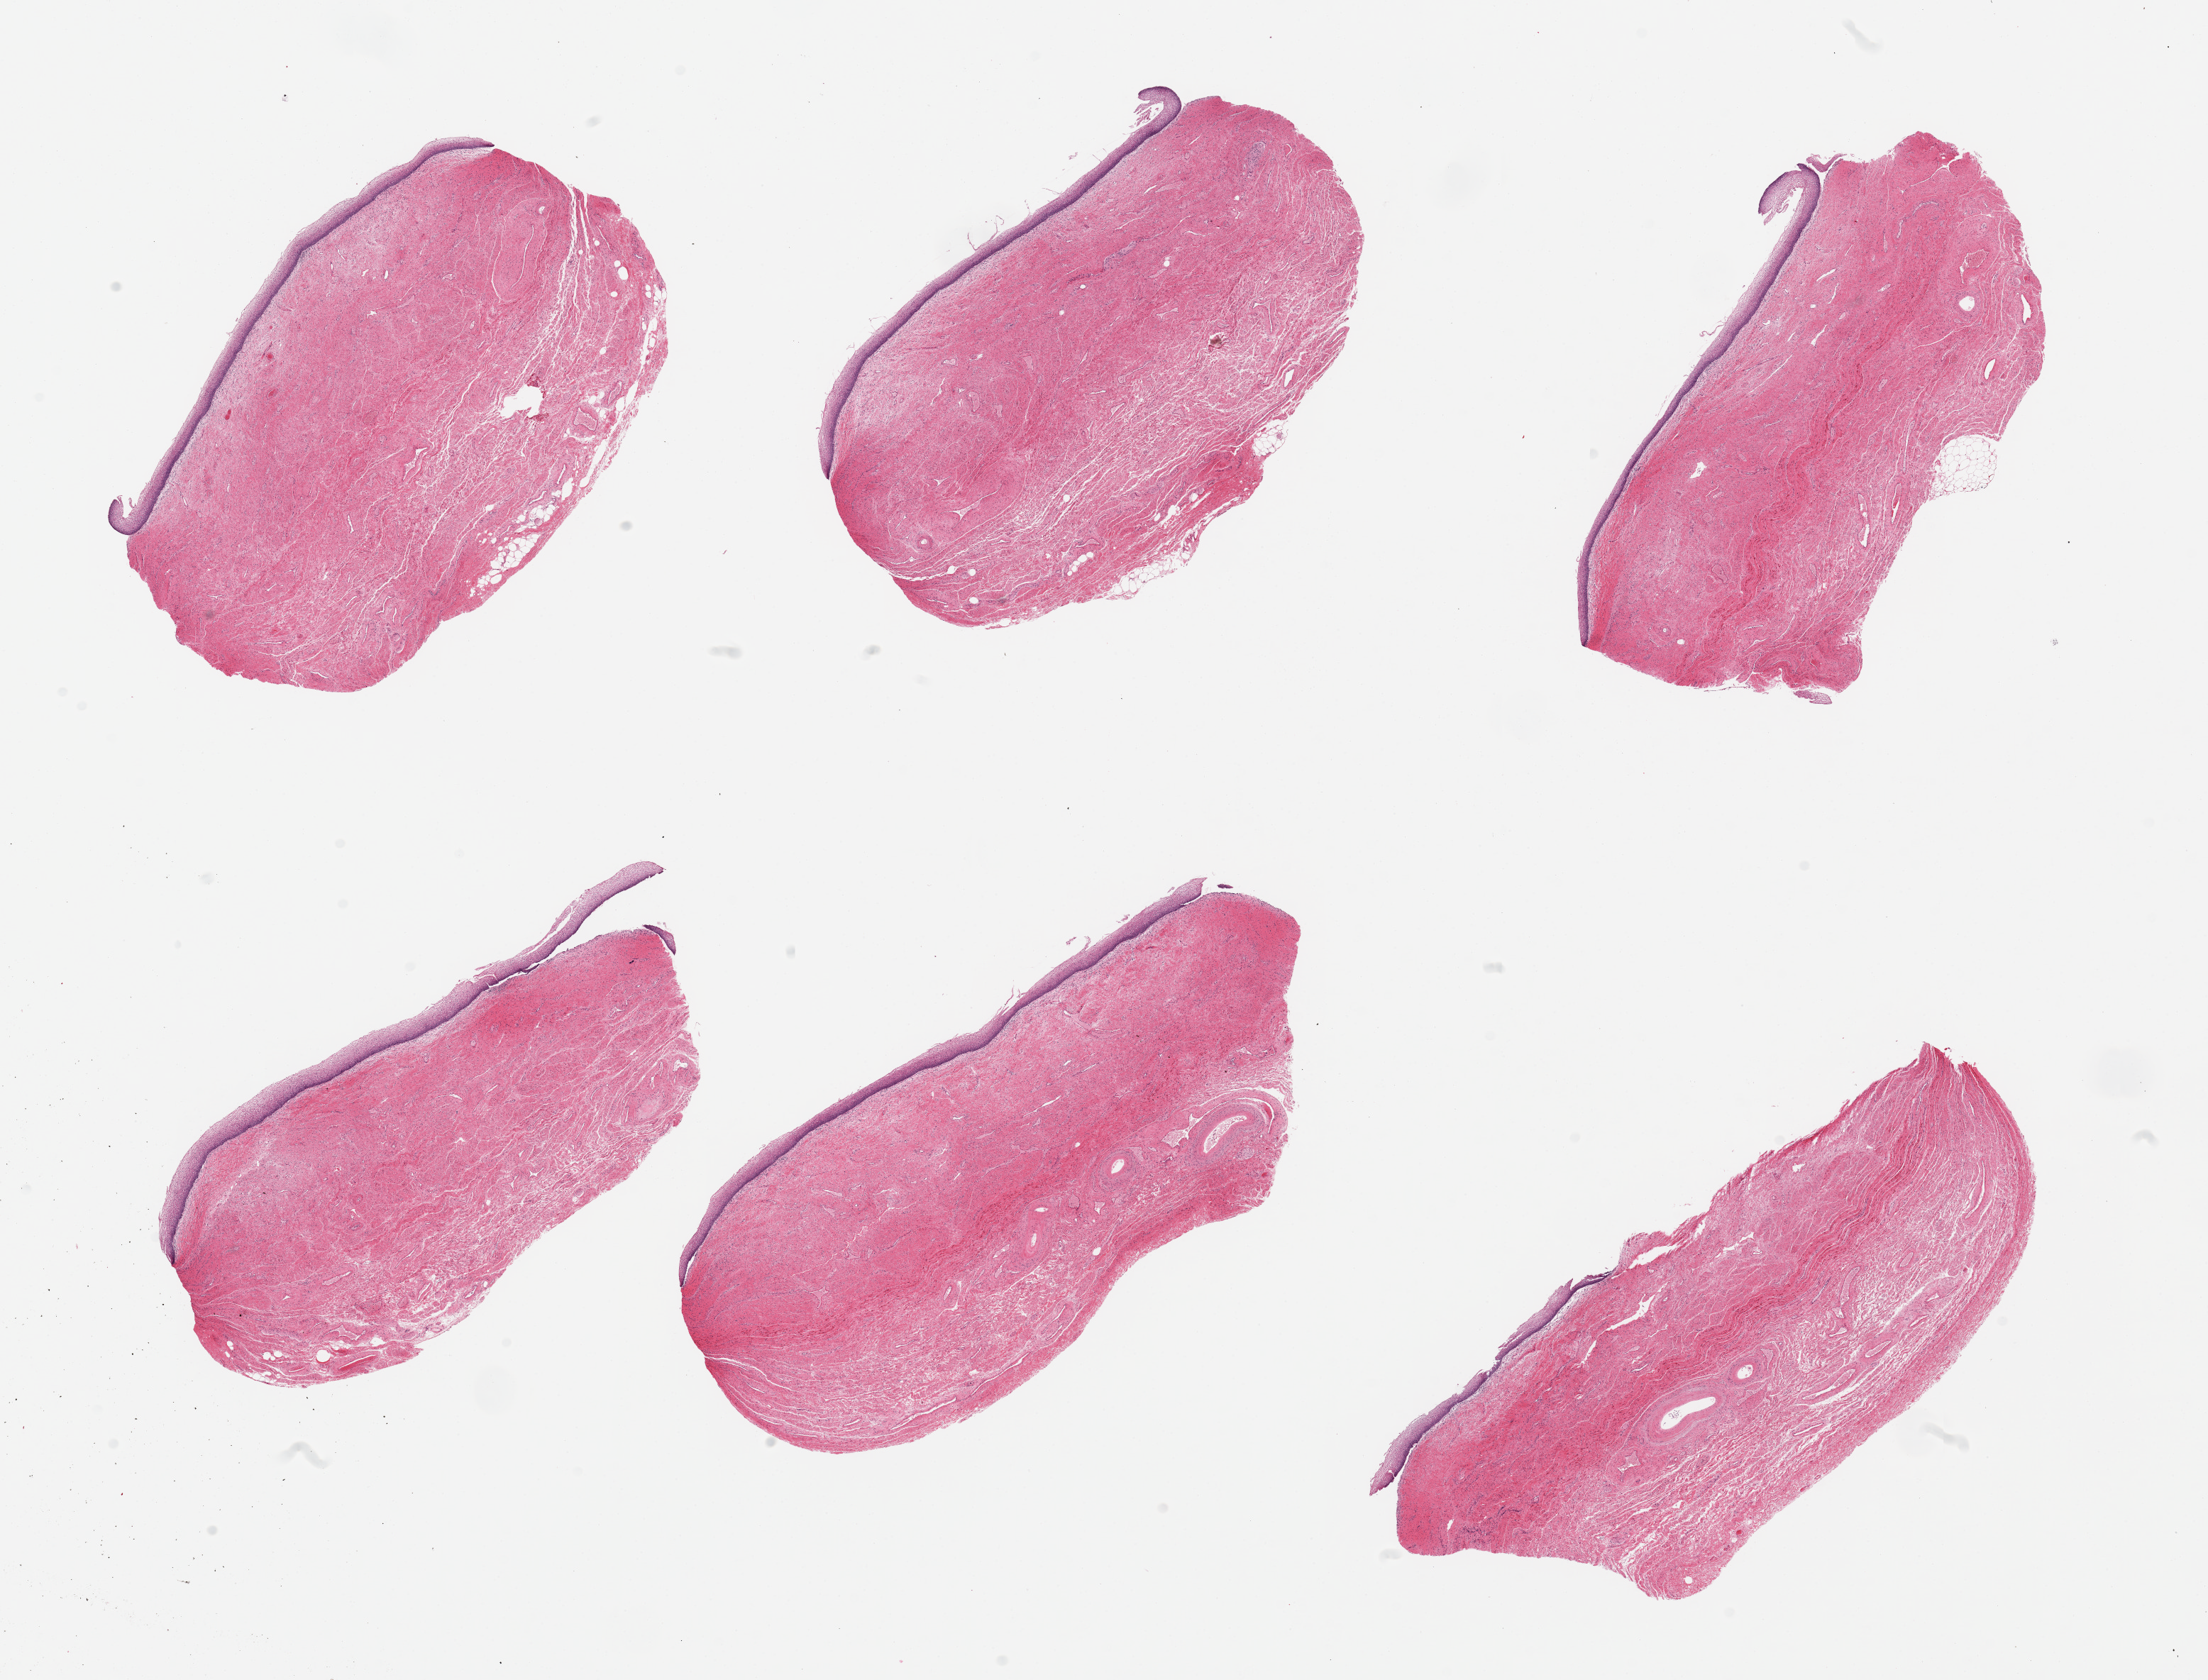
Whole-slide image, haematoxylin and eosin stain, low-resolution overview of the scanned area, about 24.6 x 18.7 mm (from a 20x scan); PAXgene-fixed paraffin-embedded (PFPE) section; target tissue: vagina; donor tissue sample. Female donor.
Pathologist's review note for this sample: 6 pieces; well trimmed.